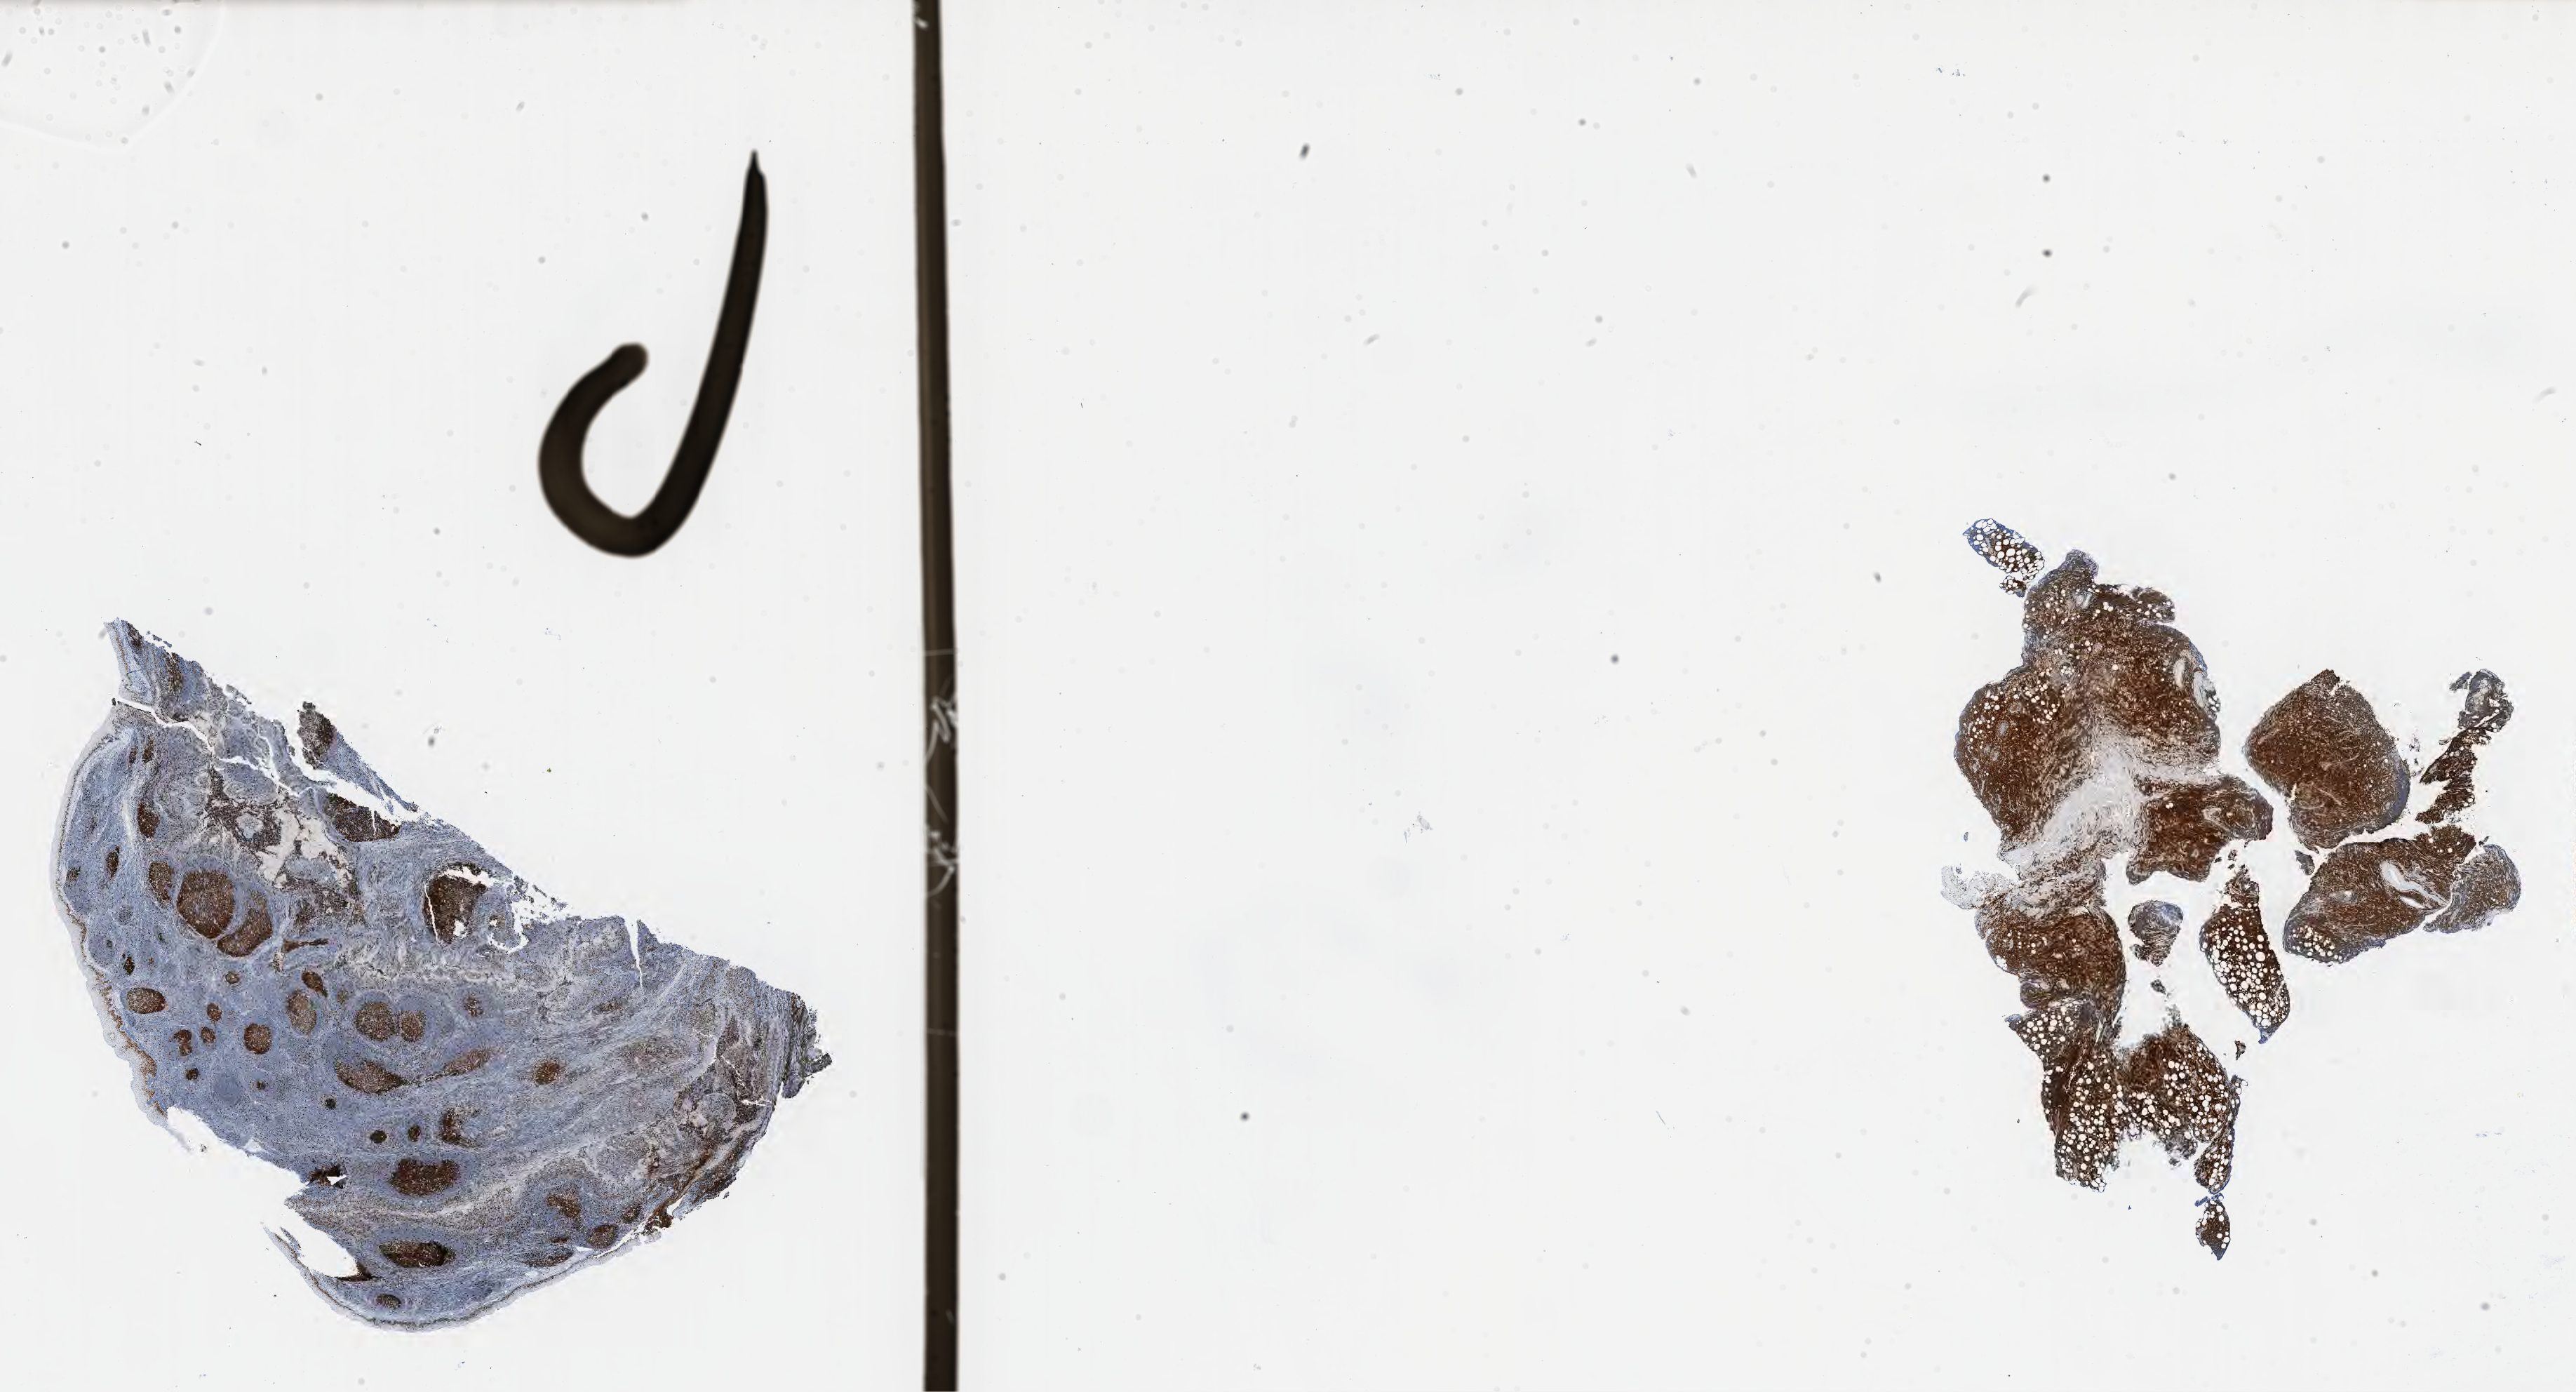
Whole-slide image, immunohistochemical stain for Ki-67, low-resolution overview of the scanned area, about 29.7 x 16.0 mm; specimen: tumor tissue; anatomic site: orbit. Patient: male, age 20 years.
Histologic diagnosis: Burkitt lymphoma, NOS.